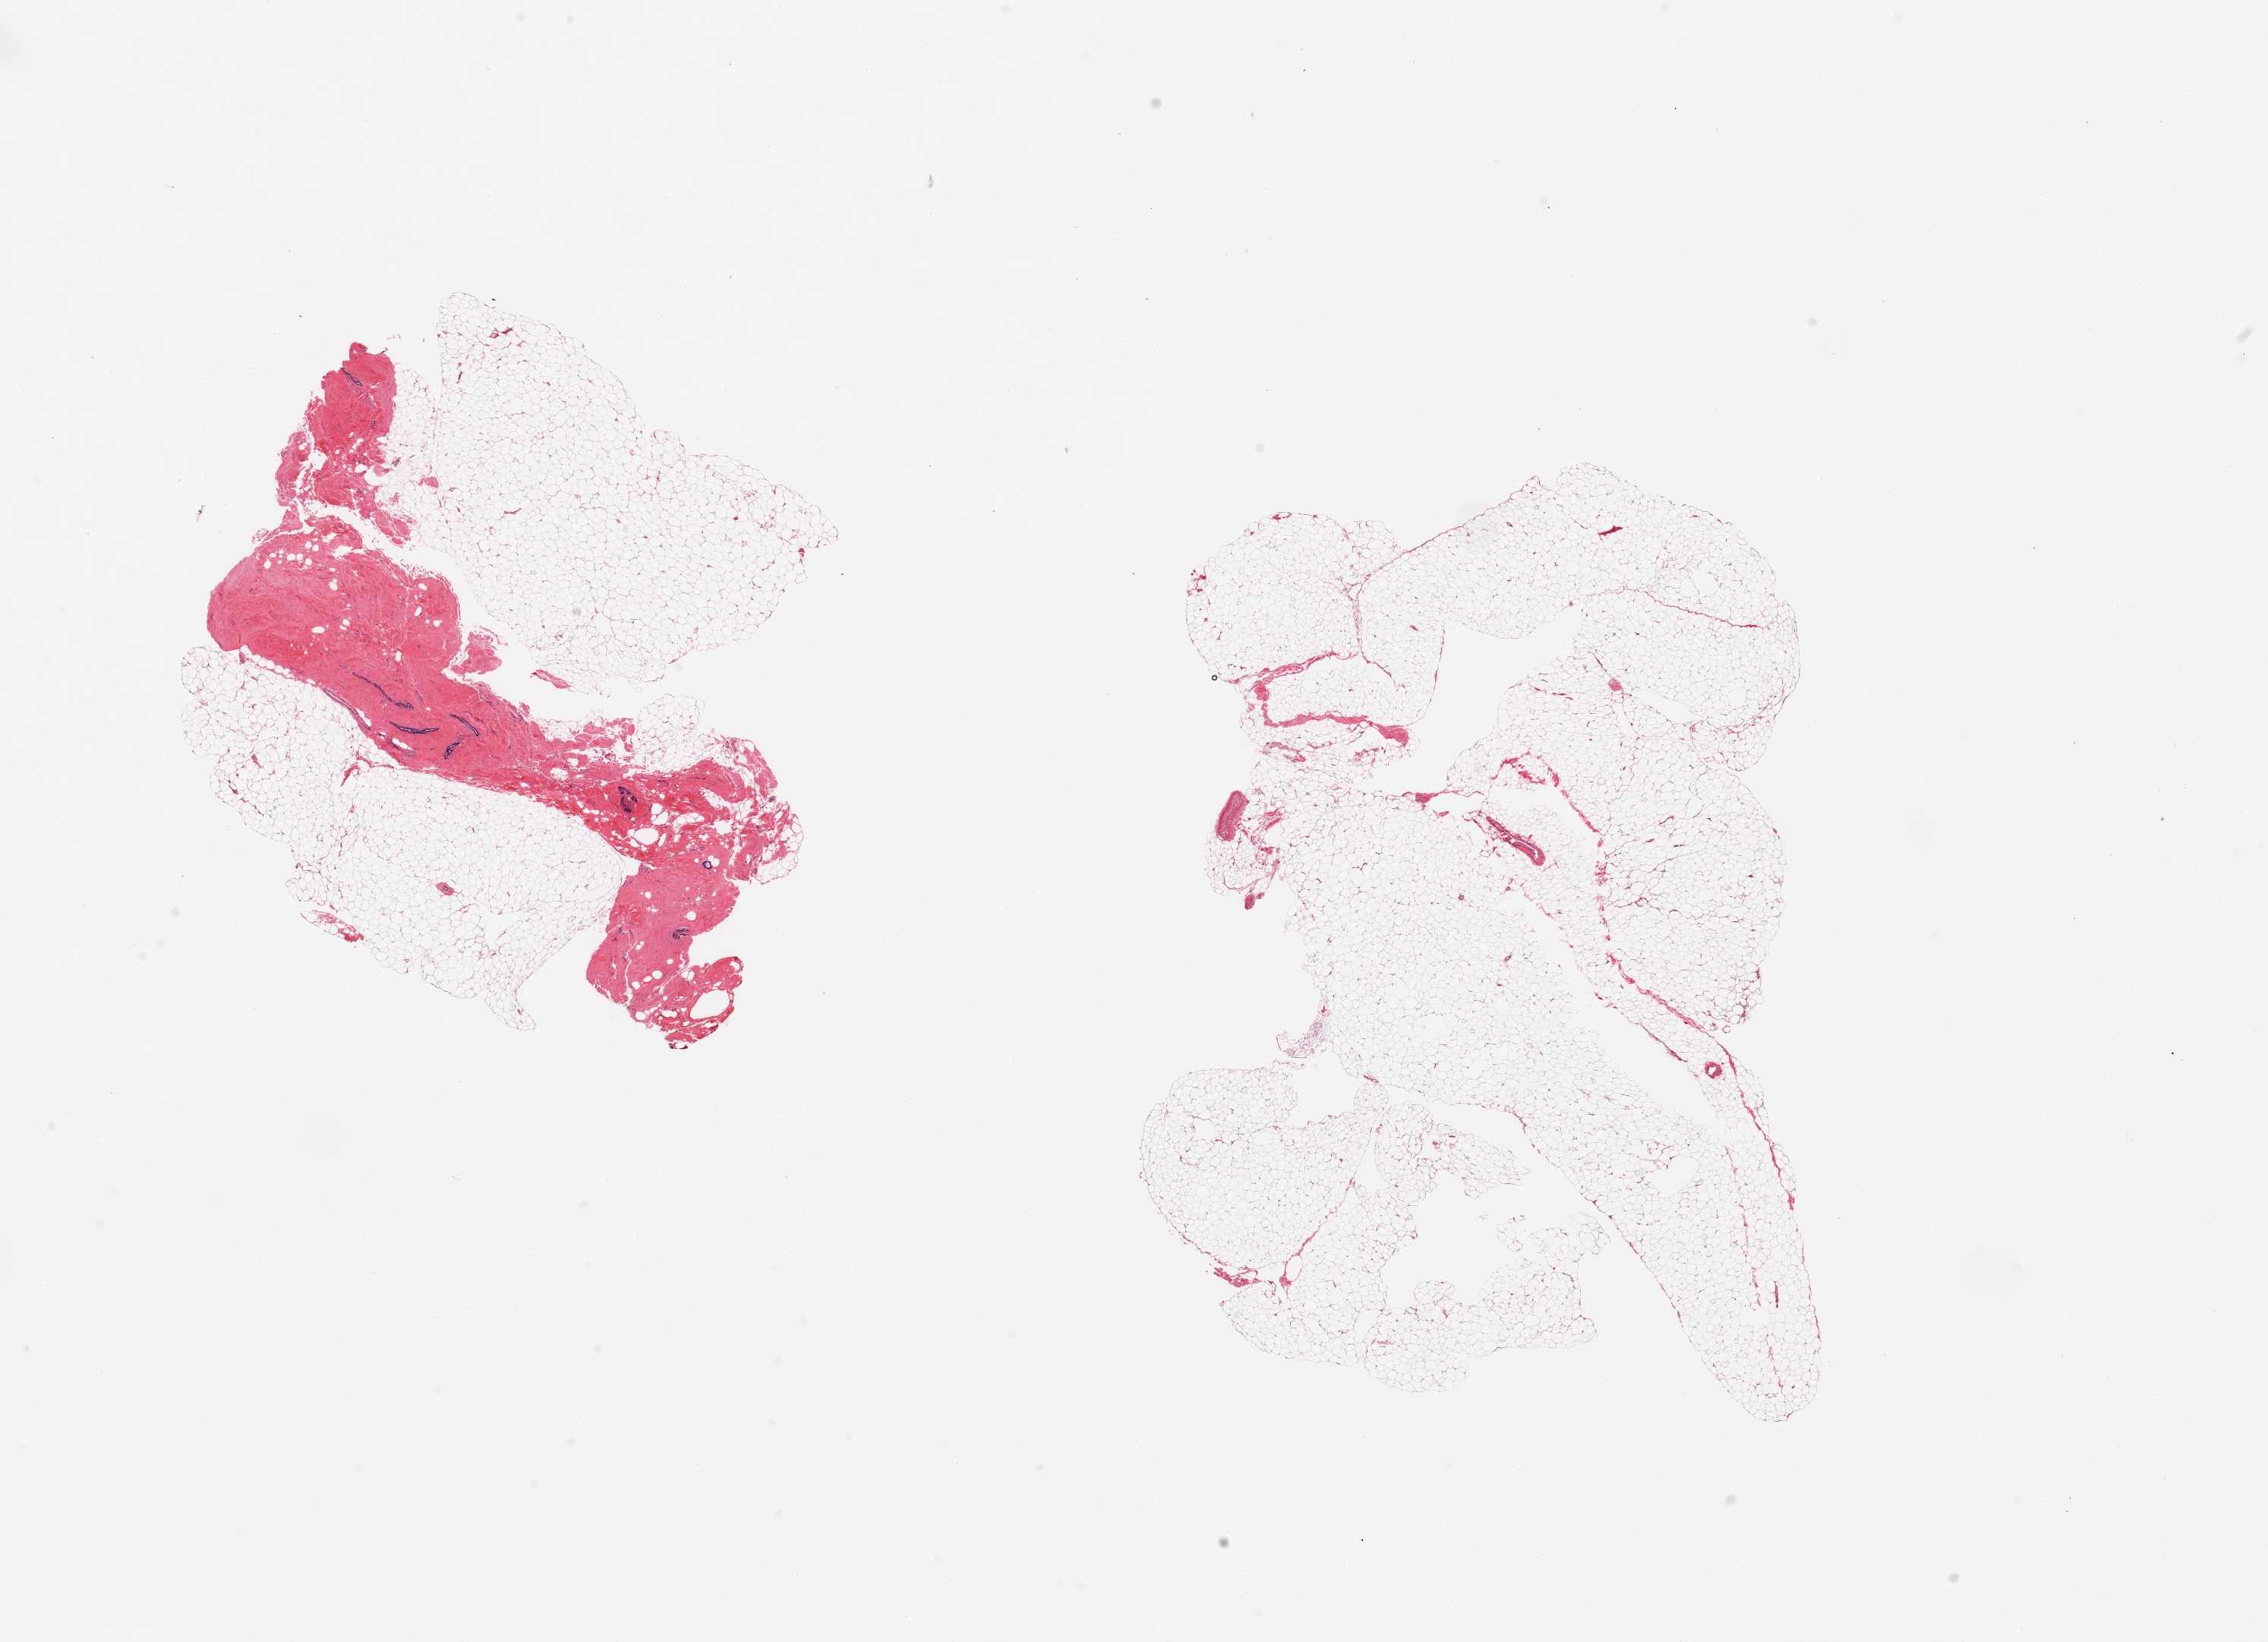
Hematoxylin and eosin (H&E) whole-slide image, whole scanned area (about 23.6 x 17.1 mm, acquisition: 20x scan) shown as a low-resolution overview, PAXgene-fixed paraffin-embedded (PFPE) section, target tissue: breast, tissue donor sample. Donor sex: male.
Review note (as recorded): 2 pieces; one piece is 60% fat with 40% dense fibrous stroma with ductal structures, second piece is fat/few vessels.